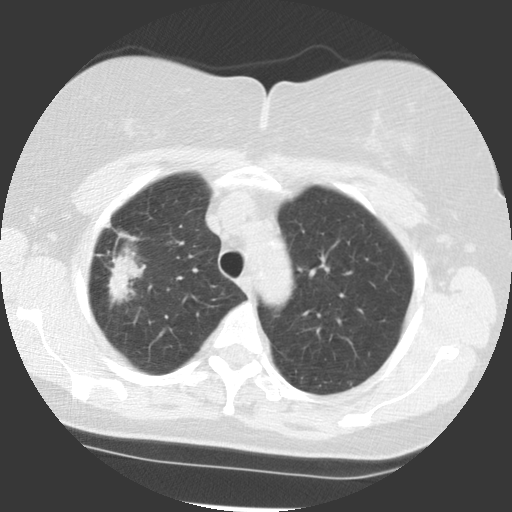
Axial slice from a low-dose chest CT screening exam, baseline annual screen, lung window (W 1500 / L -600 HU), 2.5 mm slice thickness, 140 kVp, slice 91 of 113 in the series. Female participant, aged 68 years at enrolment. Former smoker at enrolment.
Expert-annotated lung lesion, bounding box (x1, y1, x2, y2) in pixels: (90, 246, 148, 303). The exam's reader record, not a measurement of the box and not confirmed to be the same lesion: non-calcified nodule or mass ≥4 mm, right upper lobe, 42 × 20 mm, spiculated (stellate) margins, soft tissue attenuation. Official screen result: positive, change unspecified: nodule(s) >= 4 mm or enlarging nodule(s), mass(es), or other non-specific abnormalities suspicious for lung cancer. Participant outcome: lung cancer diagnosed 51 days after this screen — adenocarcinoma, NOS, right upper lobe, moderately differentiated (G2), stage IB (AJCC 6th edition), 31 mm at pathology.